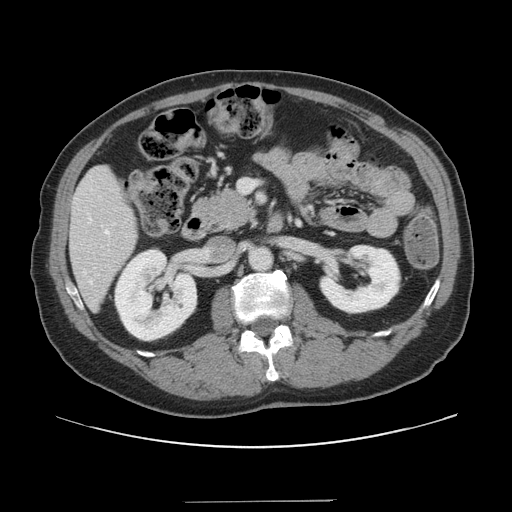
Contrast-enhanced abdominal CT, one axial slice; position 60 of 151 along the scan axis; soft-tissue window (W 400 / L 40 HU); 2.5 mm slice thickness; 512 × 512 image matrix. Male patient, age 63 years. Case-level facts recorded for this patient, not image findings: diagnosis: colorectal cancer liver metastases, imaged before liver resection; multiple liver metastases: no; largest metastasis: 2.1 cm; disease in both lobes: no.
Outlined on this slice (outlined manually by an expert reader):
- hepatic veins: bounding box <90,230,109,283> (left, top, right, bottom; pixels)
- liver: <71,167,137,308>
- planned liver remnant (the part of the liver to remain after resection): <71,167,137,308>
- portal vein (with intrahepatic branches): <239,180,256,193>